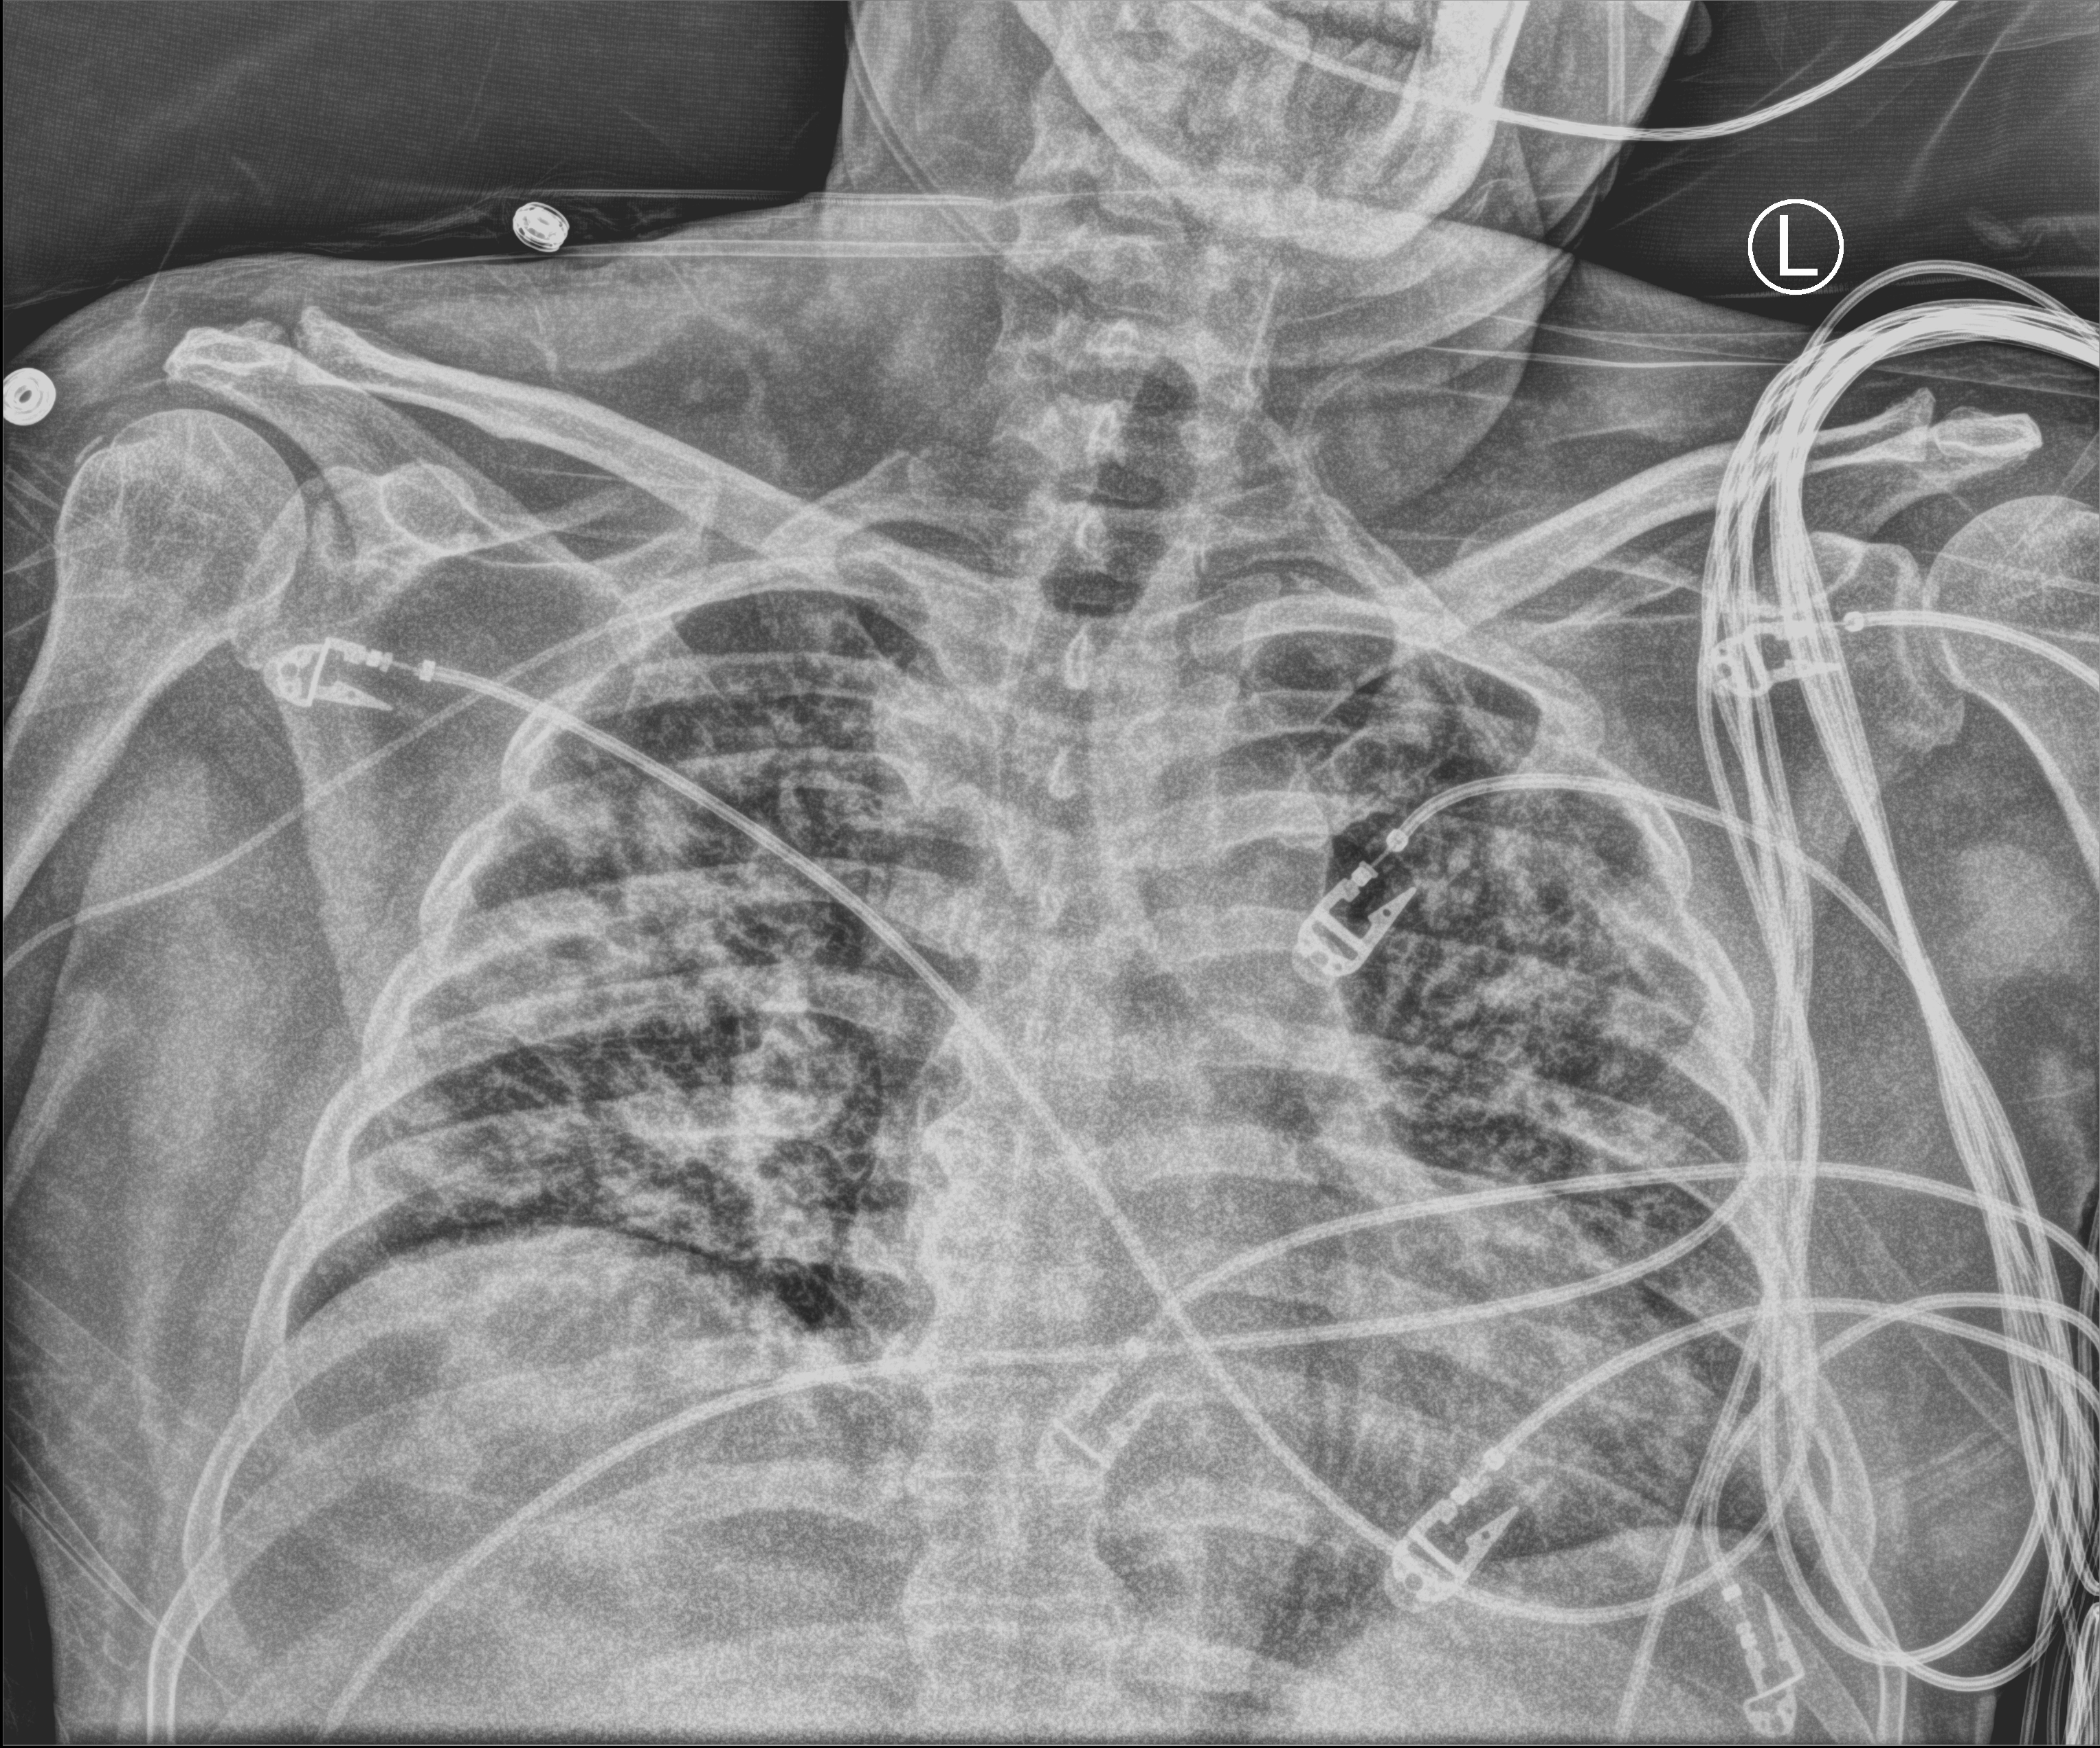
Chest X-ray (portable); anteroposterior (AP) projection. Male patient hospitalised with COVID-19, age 18–59 years.
From the hospital-stay record, not from the radiograph (when in the stay this image was taken is not recorded): hypertension (admission record): yes; admitted to intensive care during this hospital stay: yes.